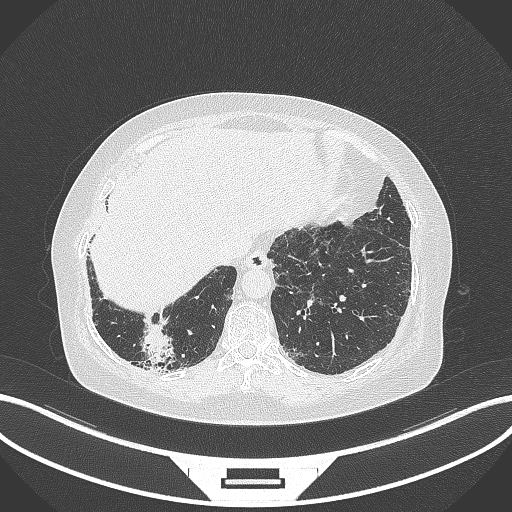
Chest CT, one axial slice; lung window (W 1500 / L -600 HU); 1 mm slice thickness; 512 × 512 image matrix. Patient: female, 65 years. From the clinical record (not read from this slice): clinical TNM (as recorded): T2b N1 M0.
Outlined on this slice (bounding box drawn by a radiologist):
- lung tumour (recorded histology: adenocarcinoma): bounding box [x1, y1, x2, y2] px = [138, 320, 177, 367]